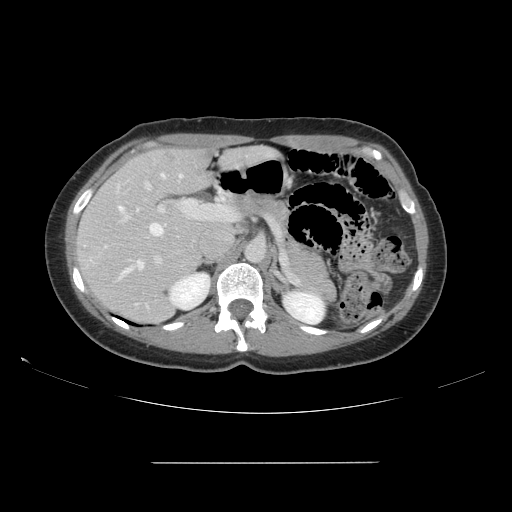
Contrast-enhanced abdominal CT, one axial slice; position 97 of 151 along the scan axis; intravenous contrast given; soft-tissue window (W 400 / L 40 HU); 512 × 512 image matrix. Female patient, age 46 years. Case-level facts recorded for this patient, not image findings: diagnosis: colorectal cancer liver metastases, imaged before liver resection; multiple liver metastases: yes; largest metastasis: 3 cm; chemotherapy before resection: no.
Annotated regions visible in this slice (expert manual segmentation):
- hepatic veins: box from (x=105, y=173) to (x=183, y=278) px
- liver: (x=77, y=149)–(x=215, y=323)
- planned liver remnant (the part of the liver to remain after resection): (x=89, y=150)–(x=212, y=258)
- portal vein (with intrahepatic branches): (x=120, y=180)–(x=234, y=265)
- liver metastasis: (x=168, y=155)–(x=177, y=163)